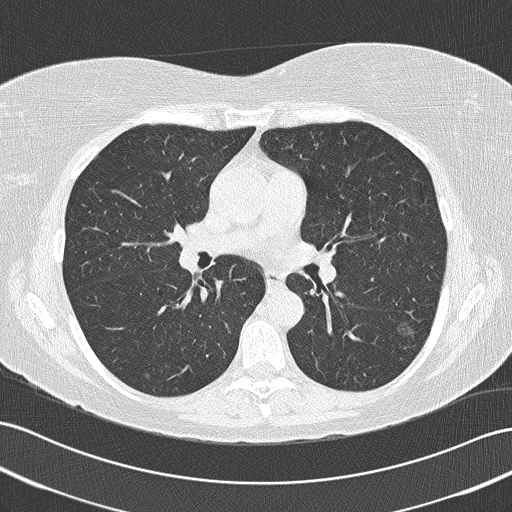
Low-dose screening chest CT, axial slice. Baseline annual screen. Lung window (W 1500 / L -600 HU). 2 mm slice thickness. Female participant, aged 57 years at enrolment. Current smoker at enrolment.
Lesion marked by an expert reader, box from (x=381, y=308) to (x=429, y=350) px. The exam's reader record, not a measurement of the box and not confirmed to be the same lesion: non-calcified nodule or mass ≥4 mm, left lower lobe, 11 × 11 mm, spiculated (stellate) margins, ground glass attenuation. Official screen result: positive, change unspecified: nodule(s) >= 4 mm or enlarging nodule(s), mass(es), or other non-specific abnormalities suspicious for lung cancer. Lung cancer was diagnosed 849 days after this screen (after the third annual screen): bronchiolo-alveolar adenocarcinoma, NOS, left lower lobe, well differentiated (G1), stage IA (AJCC 6th edition), 16 mm at pathology.